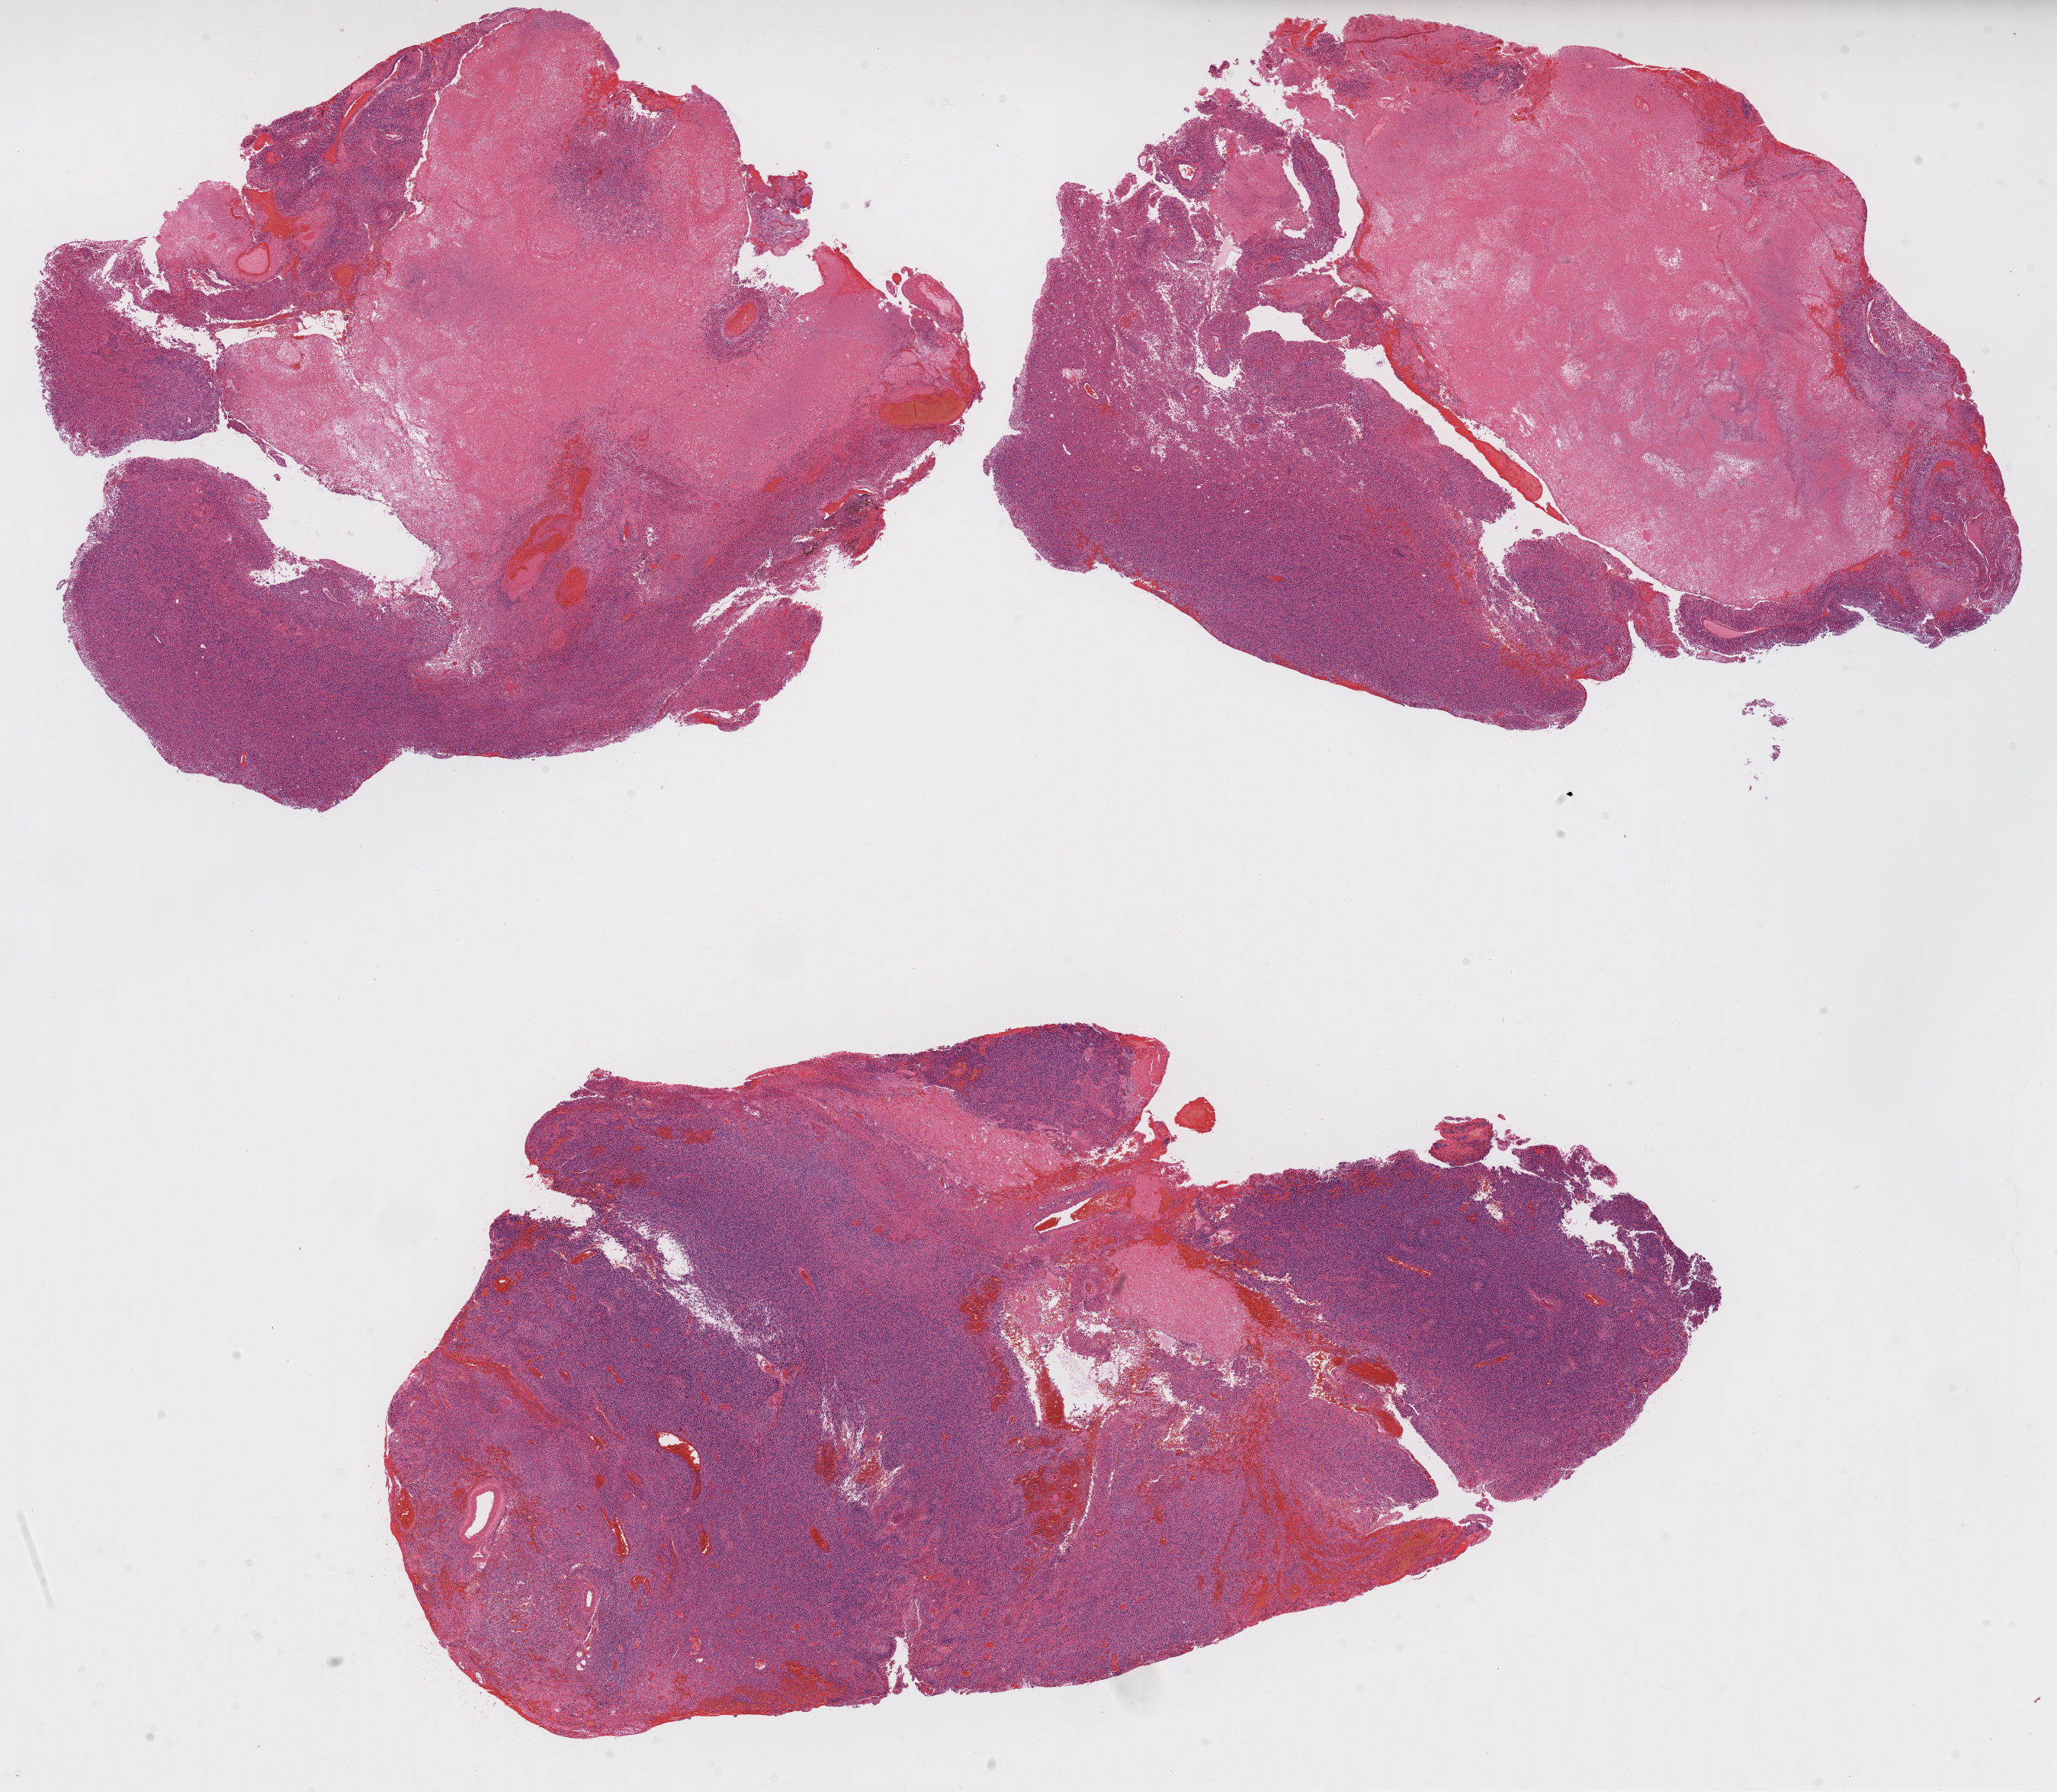
Whole-slide histology image, Hematoxylin and eosin (H&E) stained, low-resolution overview of the scanned area, about 21.8 x 19.0 mm, formalin-fixed paraffin-embedded (FFPE) diagnostic section, primary tumour sample from the brain. Patient: female, age at initial diagnosis 61 years.
* diagnosis: Glioblastoma